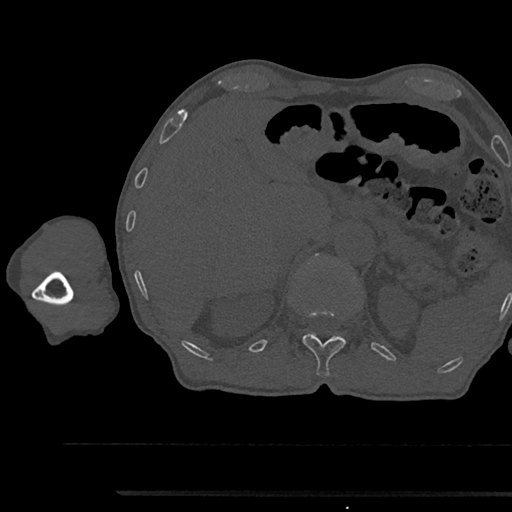
CT including the spine, one axial slice; slice 692 of 797 in the series (ordered by position); 120 kVp; bone window (W 1800 / L 400 HU); 0.5 mm slice thickness; 512 × 512 image matrix, field of view 367 × 367 mm. Patient: male, 79 years. Case-level facts recorded for this patient, not image findings: primary cancer: prostate.
Structures marked on this image (semi-automatically segmented with operator editing):
- T12 vertebra: bounding box <302,312,346,376> (left, top, right, bottom; pixels)